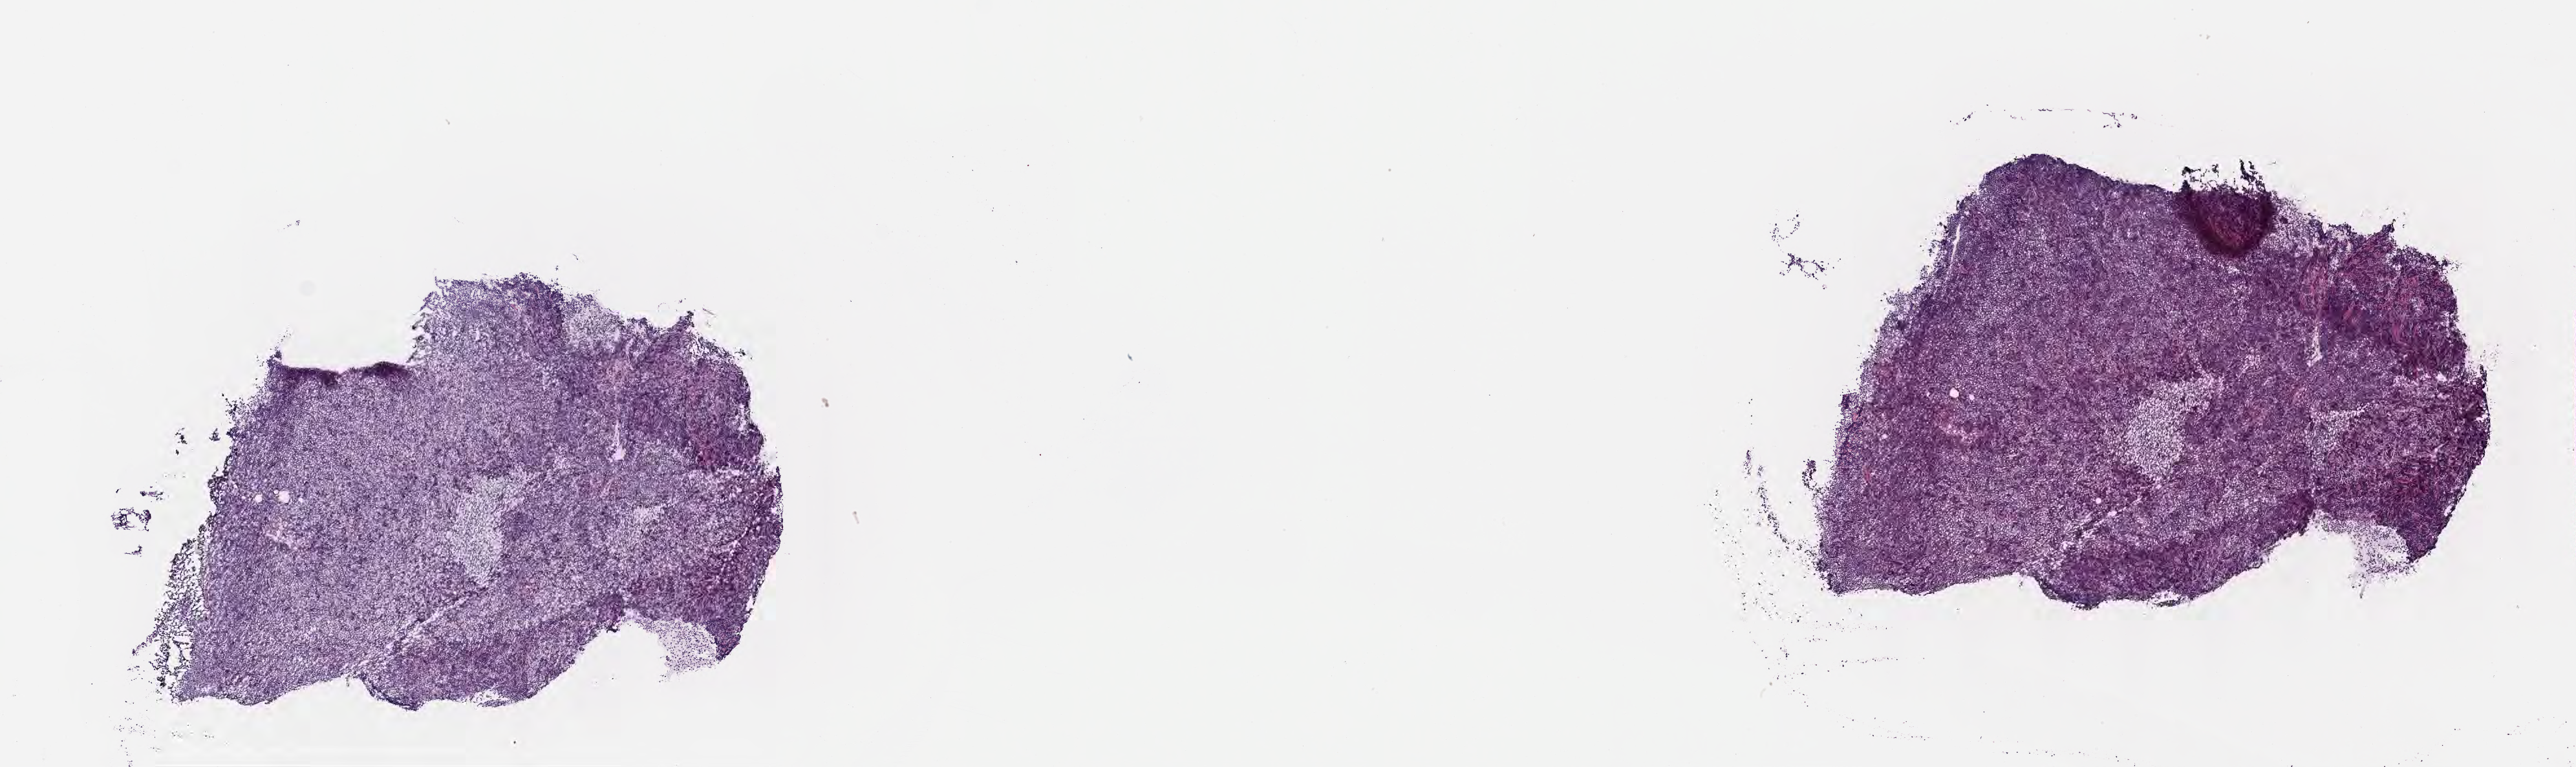
Digitized hematoxylin and eosin (H&E)-stained section — shown as a low-resolution overview of the whole scanned area (about 16.1 x 4.8 mm). Frozen section (tissue freezing medium). Primary tumor. Site: cranium. Male patient; age at initial diagnosis 2 years. Pathologist review of this section (percent, as recorded): tumor cells 85%, tumor nuclei 90%, stromal cells 10%, necrosis 5%, normal cells 0%. Infiltration values recorded for this section: lymphocyte infiltration 70%, monocyte infiltration 15%, neutrophil infiltration 0%.
Diagnosis: Burkitt lymphoma, NOS. Ann Arbor stage (patient): Stage IV. Section: top of the tissue portion.